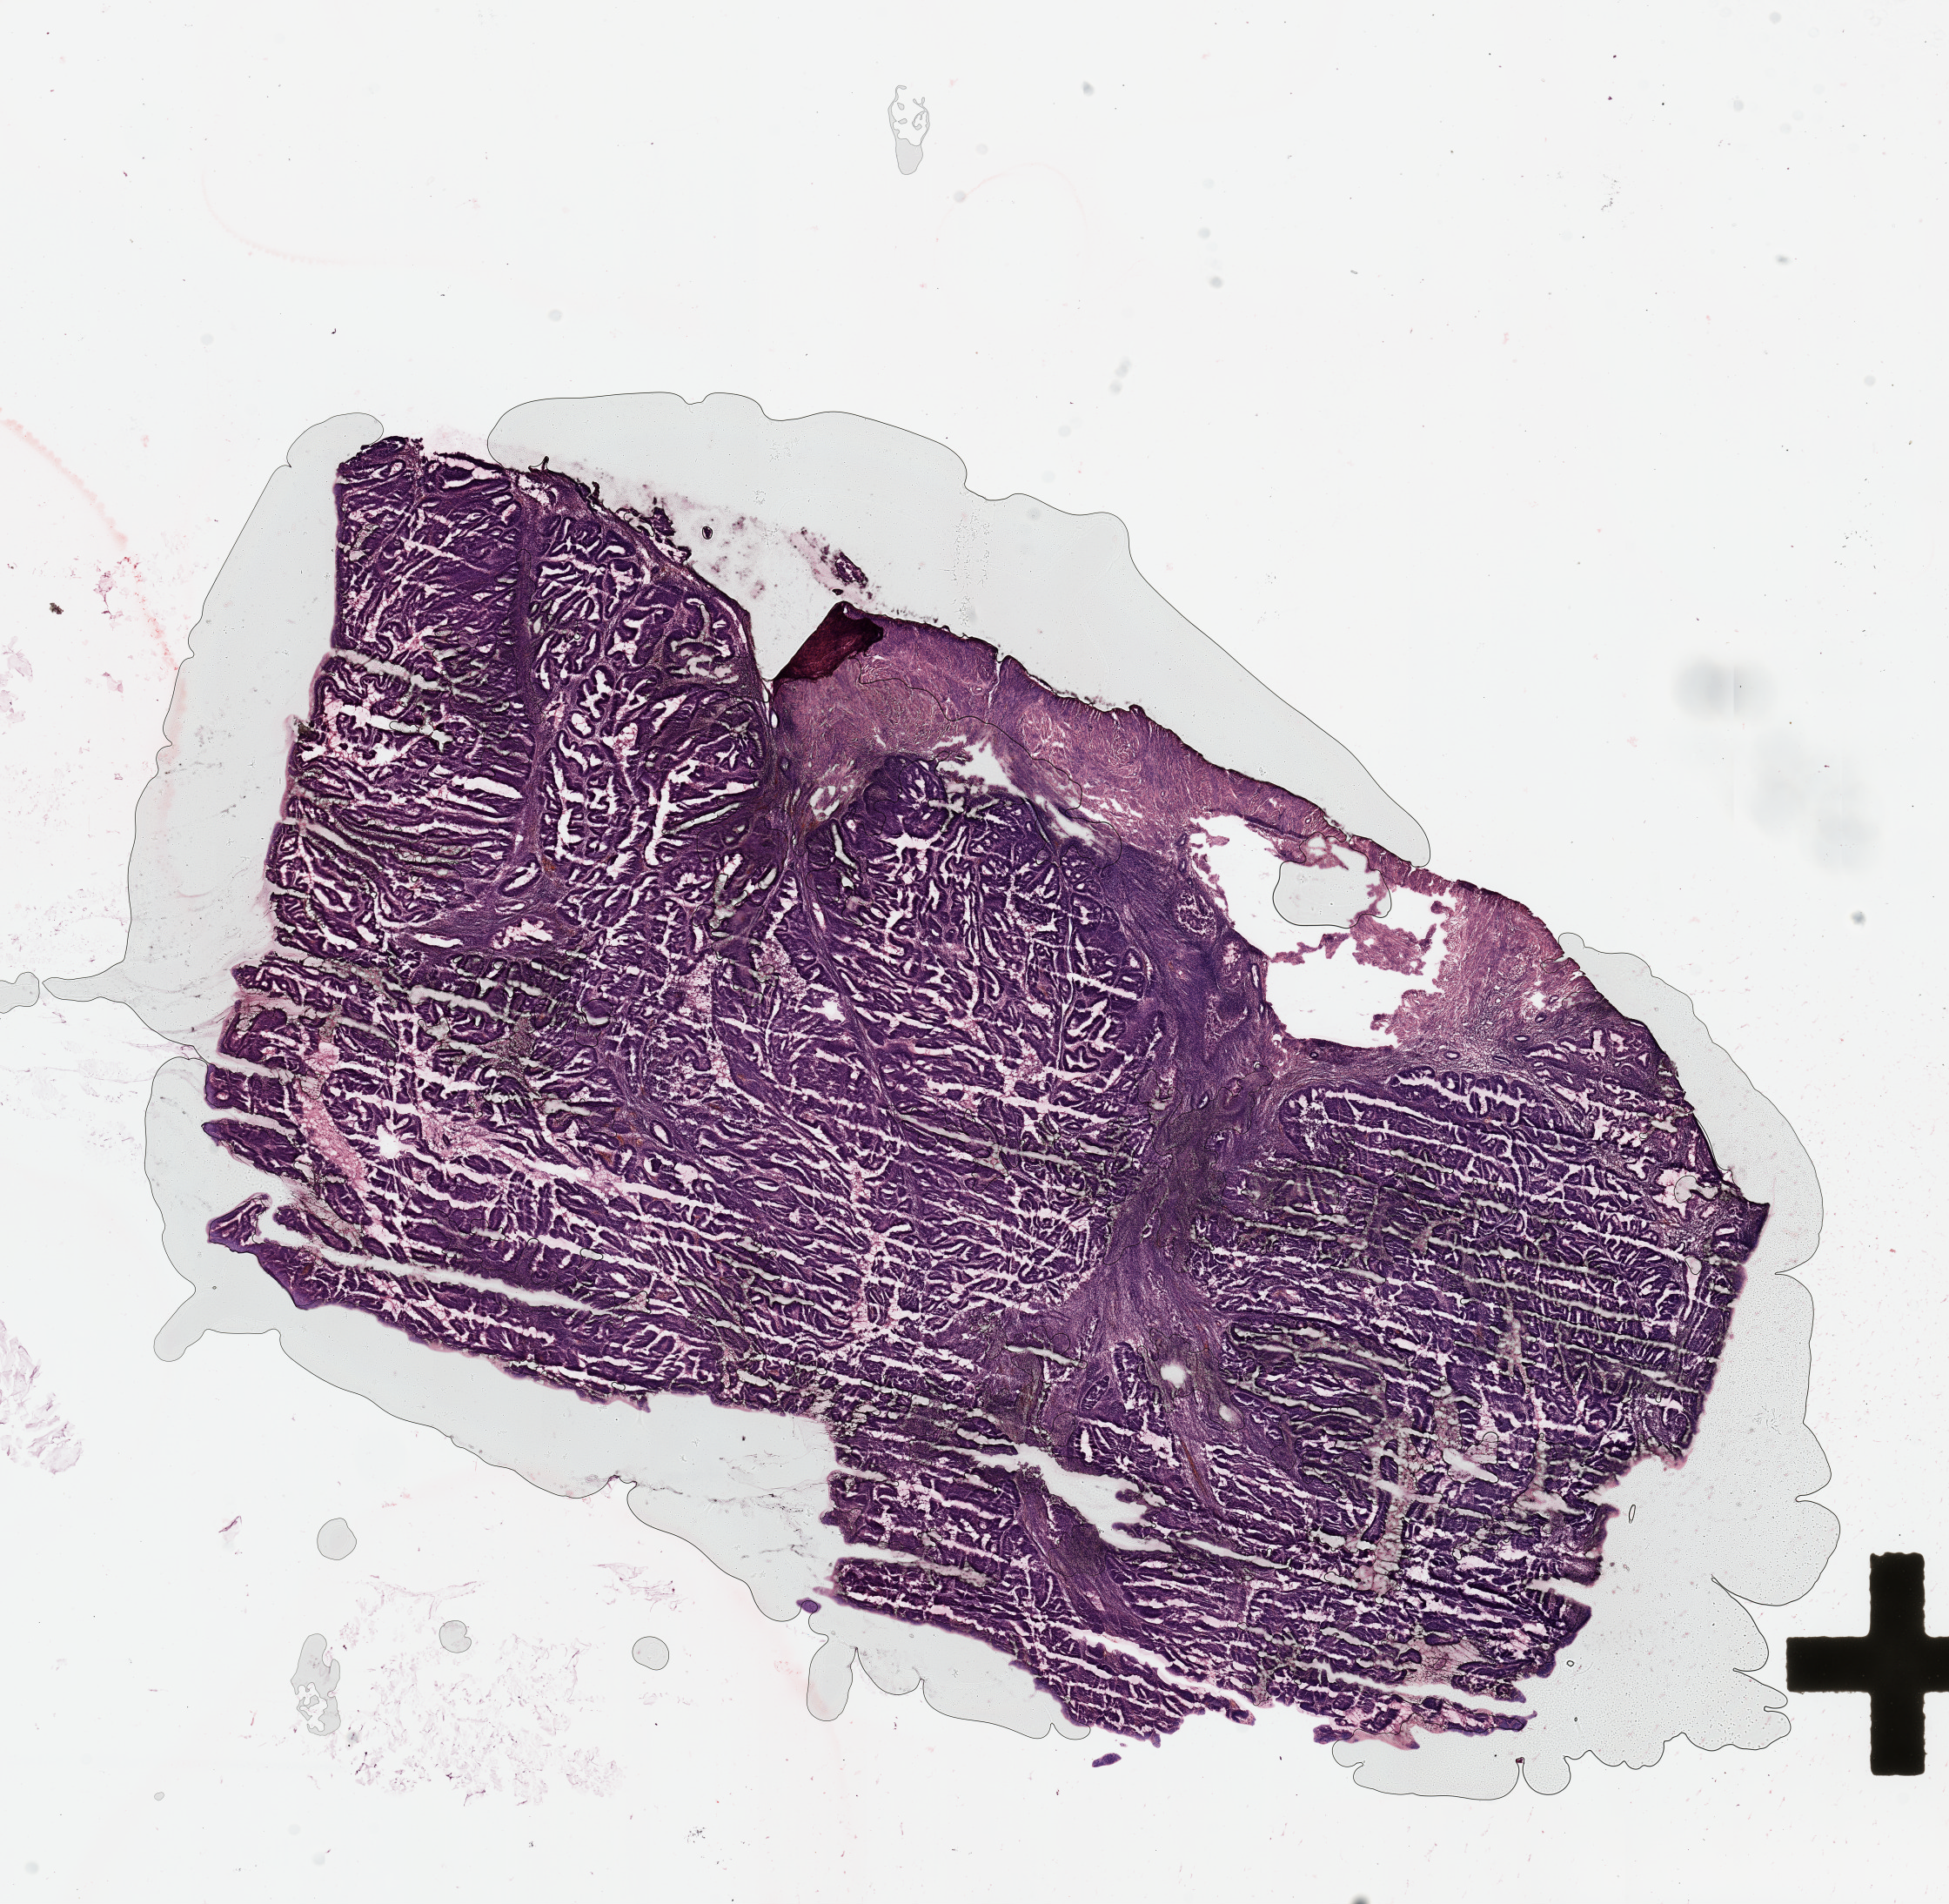
Digitized H&E-stained tissue section (whole slide) — whole scanned area (about 17.7 x 17.3 mm, from a 20x scan) shown as a low-resolution overview; uterus, tumour tissue. 45-year-old female patient. Histologic grade: G1 (well differentiated).
• AJCC pathologic stage: I
• histologic diagnosis: Endometrioid adenocarcinoma, NOS